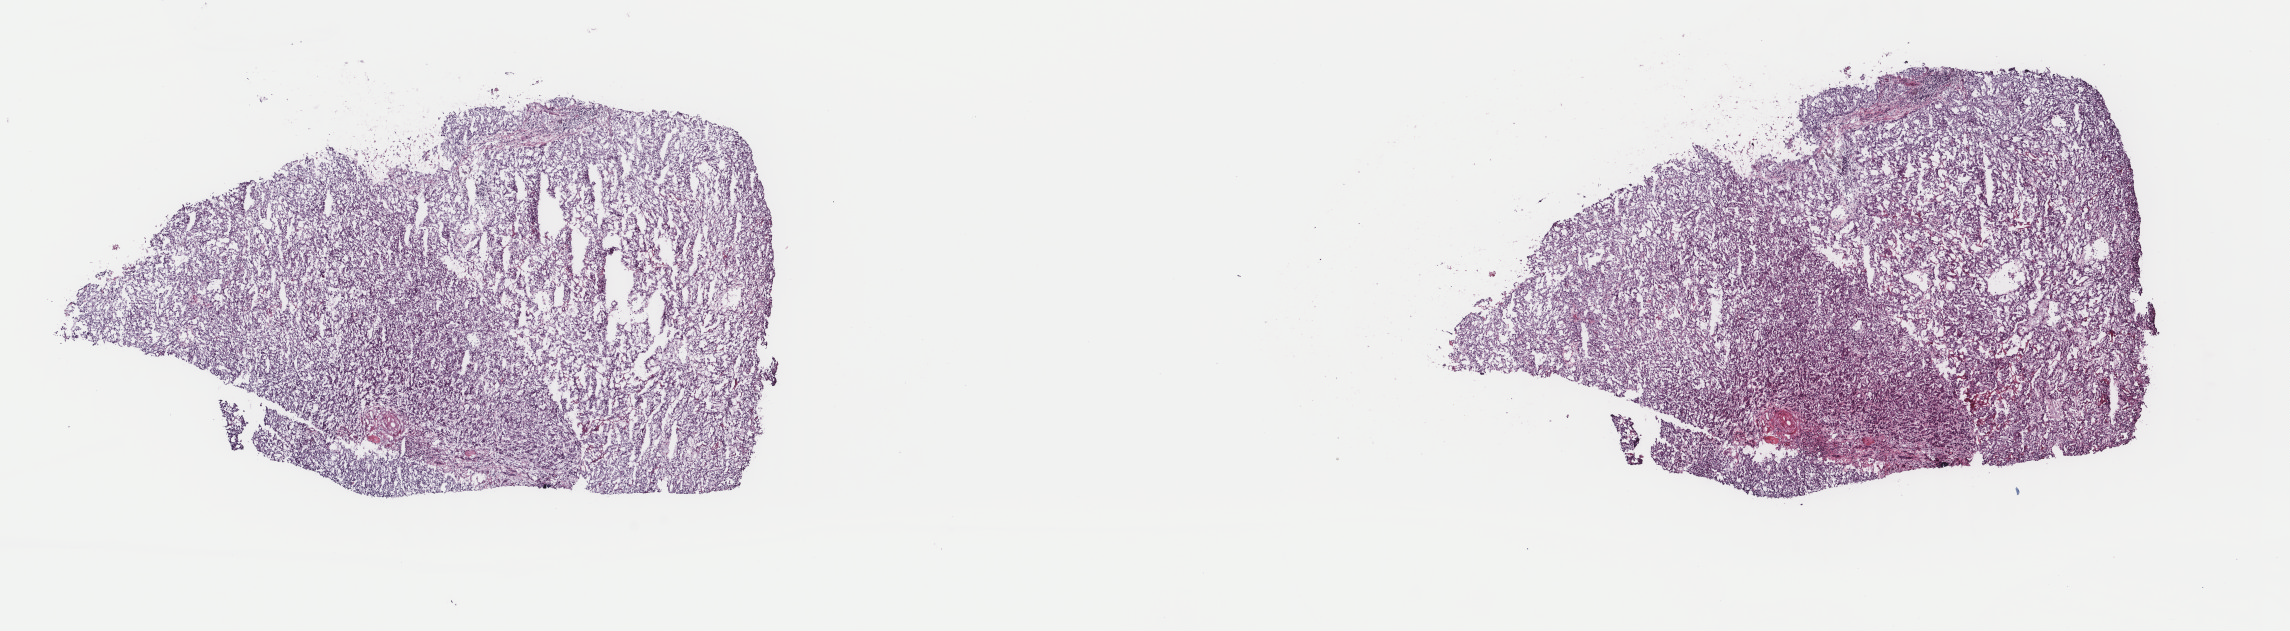
Digitized H&E tissue section (whole slide) — a low-resolution overview of the entire scanned area, about 18.2 x 5.0 mm (slide scanned at 40x). Frozen section. Kidney, primary tumour sample. Female patient; age at initial diagnosis 74 years. Composition of this section per pathologist review: tumour cells 100%, tumour nuclei 80%, normal cells 0%, stromal cells 0%, necrosis 0%. Infiltration values recorded for this section: lymphocyte infiltration 4%, monocyte infiltration 0%, neutrophil infiltration 0%.
* AJCC pathologic stage: I (7th edition)
* diagnosis: Papillary adenocarcinoma, NOS
* laterality: left